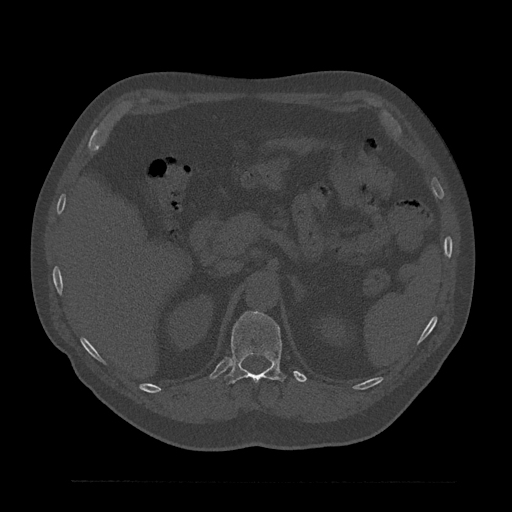
CT including the spine, one axial slice. Slice 230 of 797 in the series (ordered by position). Reconstruction kernel Br40s/3. 120 kVp. Bone window (W 1800 / L 400 HU). 0.5 mm slice thickness. 512 × 512 image matrix, field of view 430 × 430 mm. Male patient, age 61 years. Case-level facts recorded for this patient, not image findings: primary cancer: prostate.
Structures marked on this image (semi-automatic segmentation, software-assisted and operator-edited):
- T12 vertebra: box from (x=225, y=312) to (x=286, y=384) px